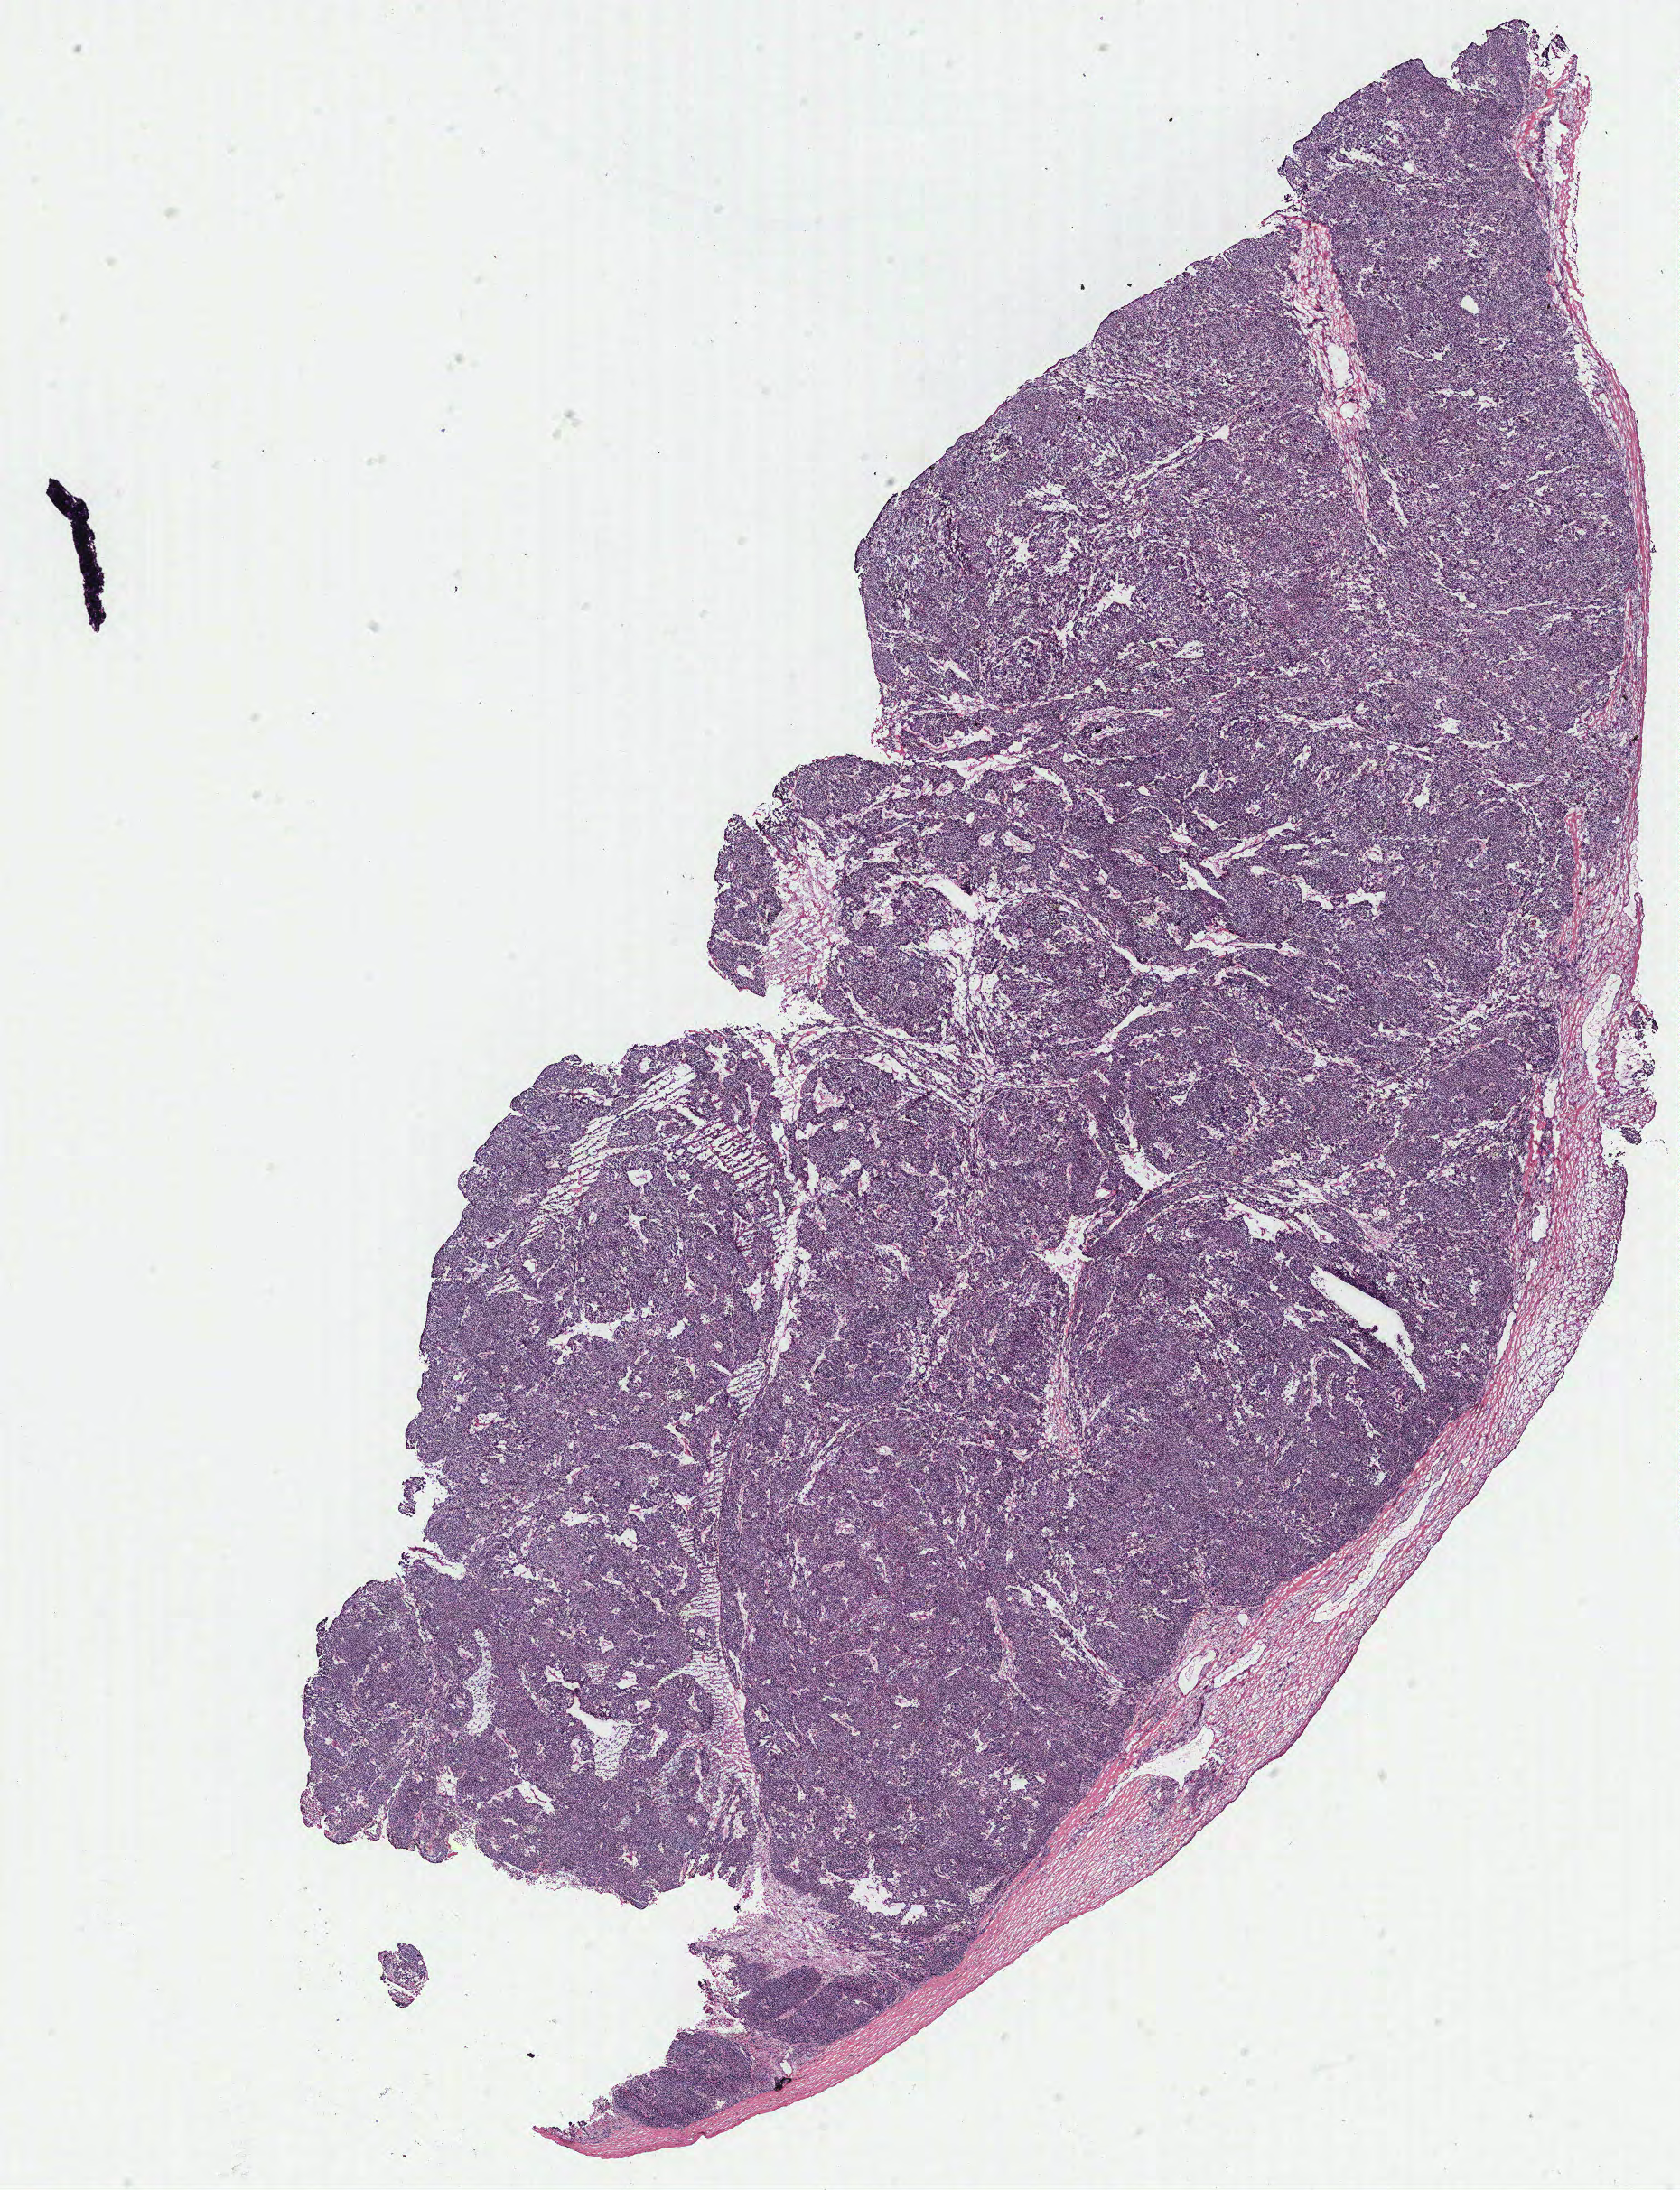
Whole-slide histology image, H&E, low-resolution overview of the scanned area, about 14.9 x 19.4 mm (slide scanned at 40x), tumour tissue sample, ovary. Female, 51 y/o.
Histologic diagnosis: Serous adenocarcinoma, NOS.